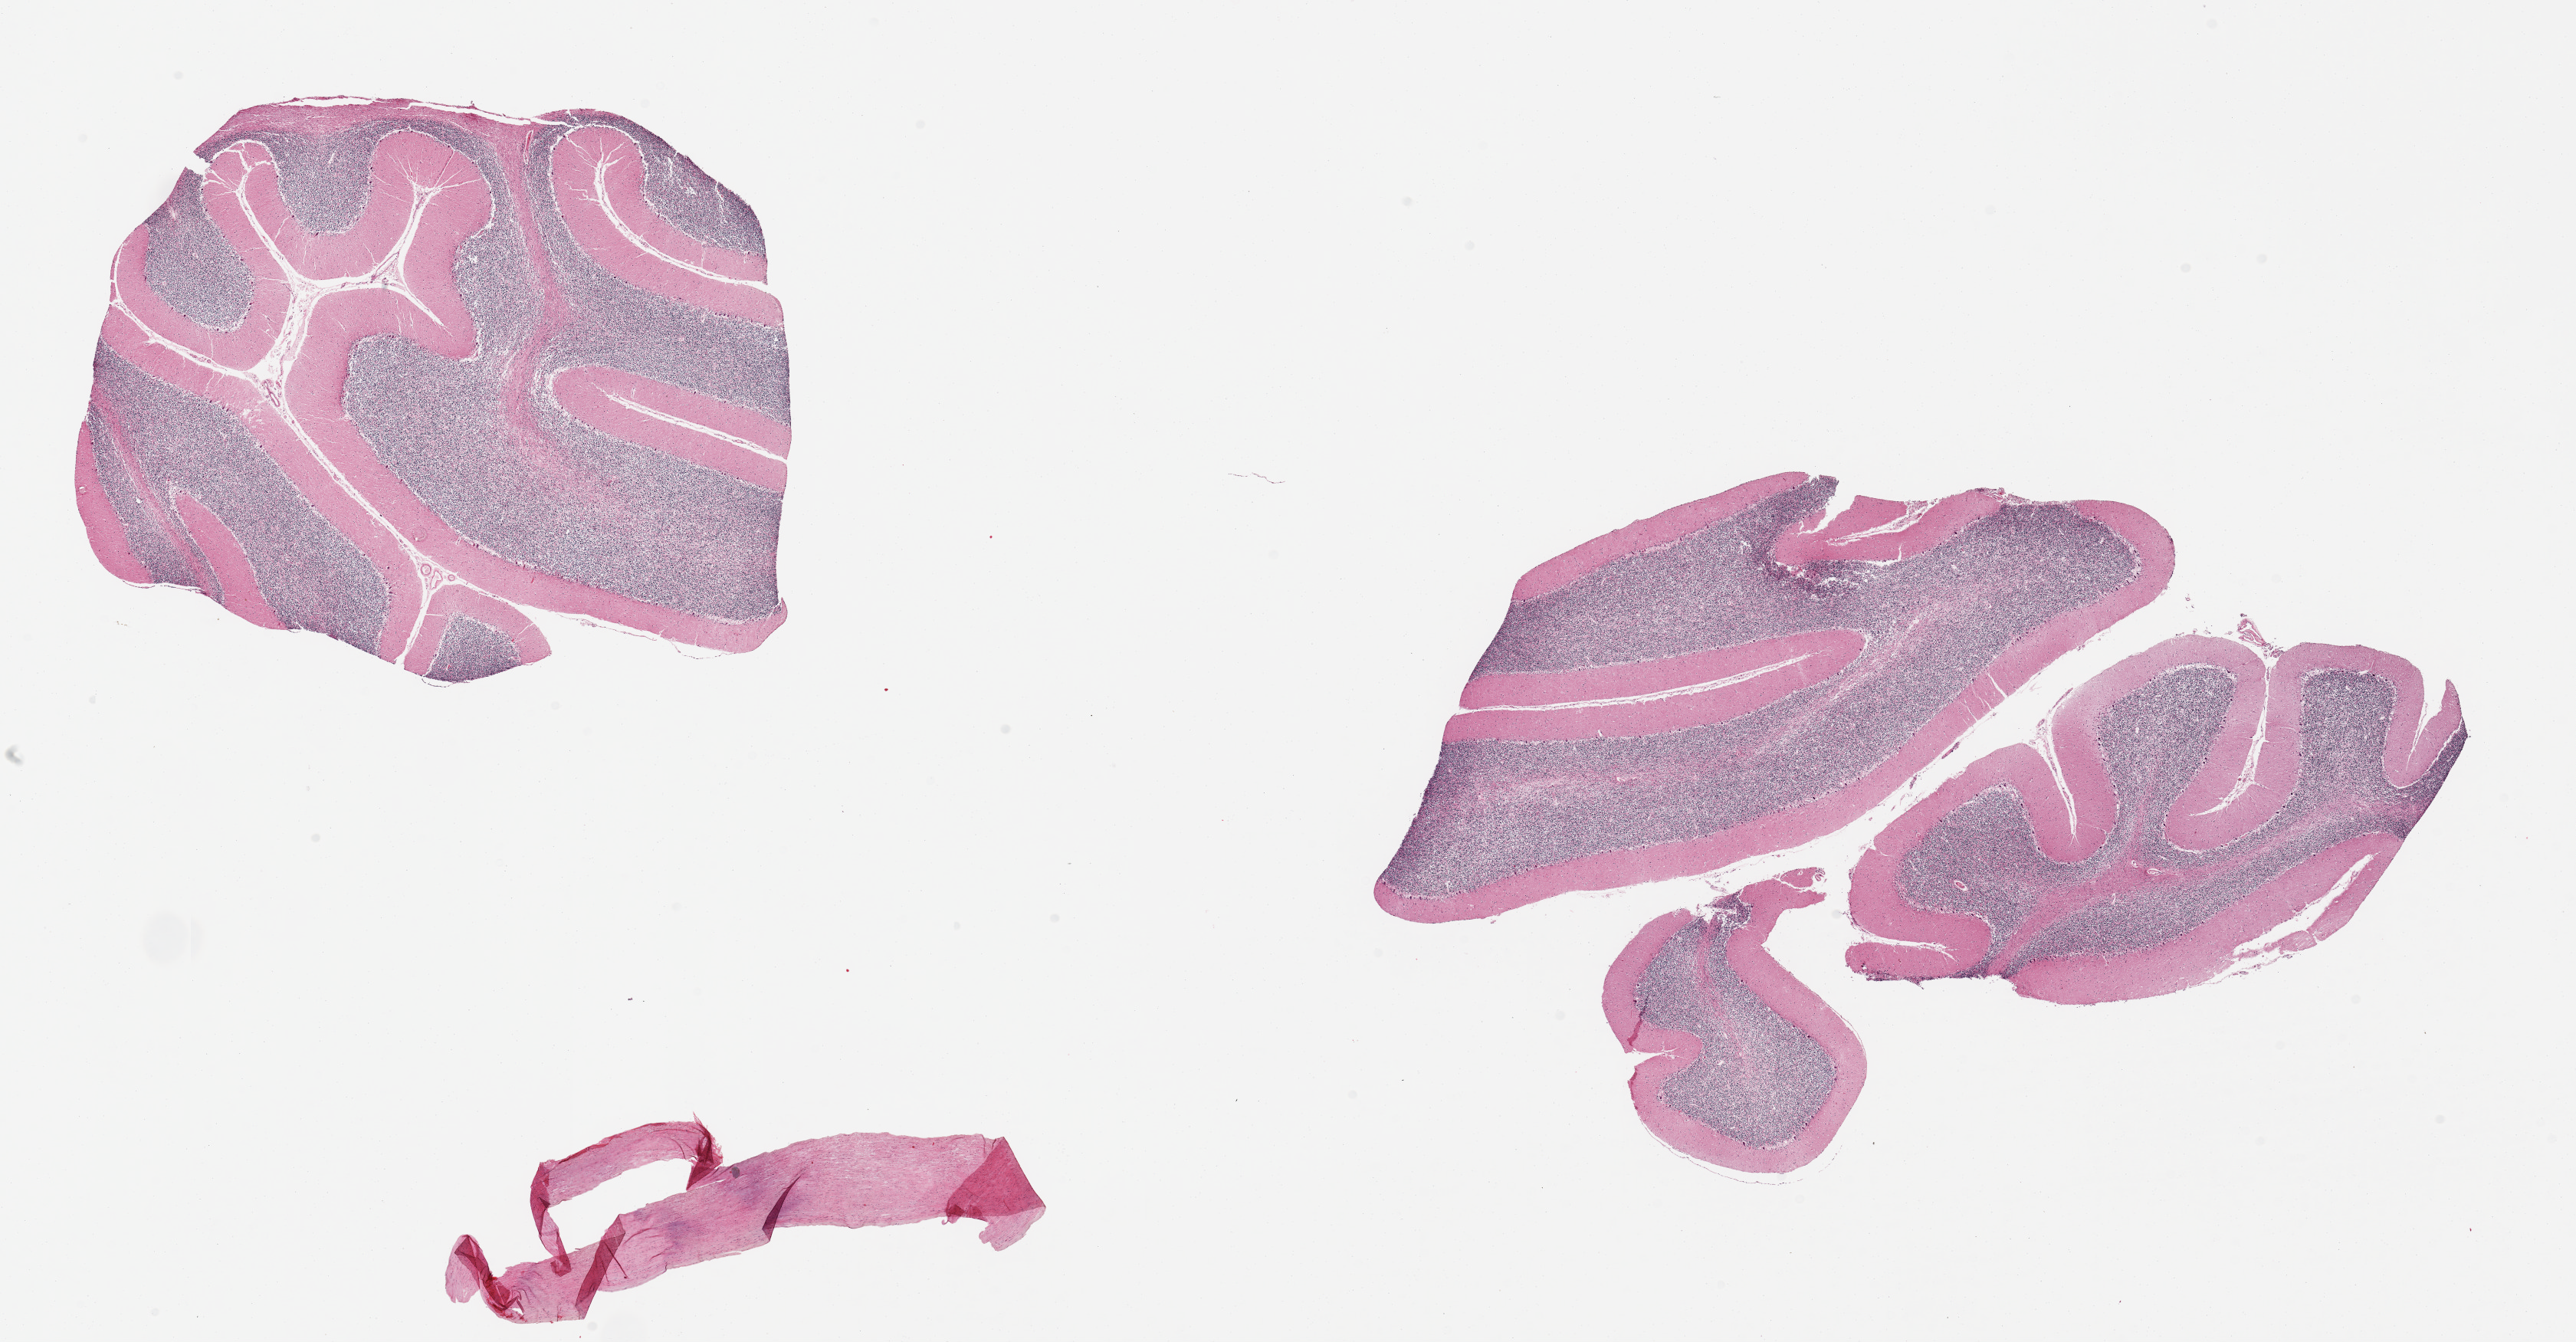
Whole-slide image, H&E stain — low-resolution overview of the scanned area, about 26.6 x 13.8 mm (acquisition: 20x scan). PAXgene-fixed paraffin-embedded (PFPE) section. Target tissue: cerebellum. Donor tissue sample. Male donor.
- pathologist's review note for this sample: 2 pieces, no abnormalities